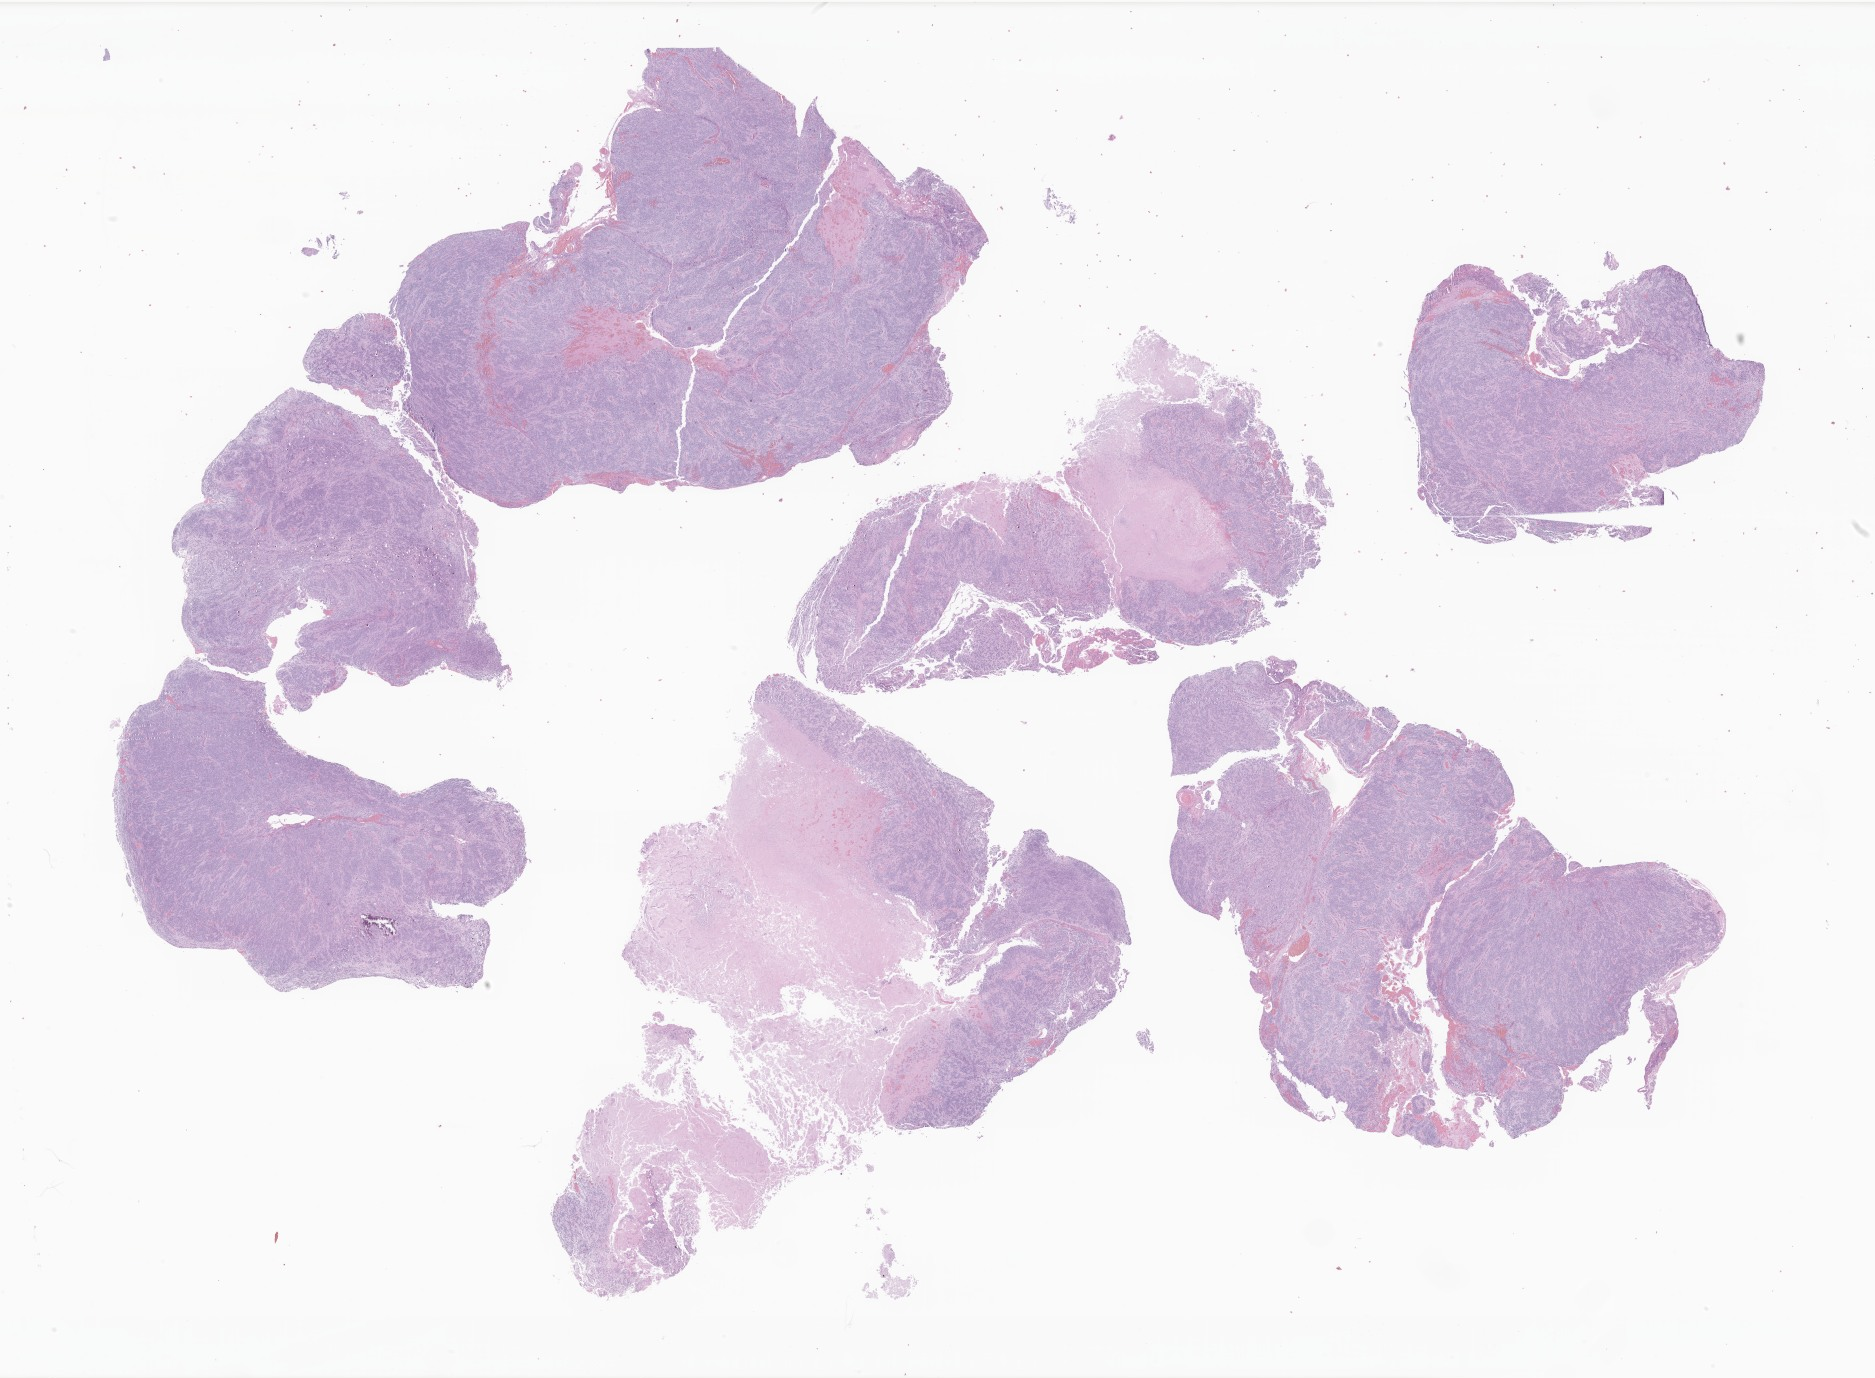
Haematoxylin and eosin whole-slide image of tumor tissue from the brain — whole scanned area (about 31.6 x 23.2 mm) shown as a low-resolution overview, formalin-fixed paraffin-embedded section. Patient: male, age 143 months (11 years 11 months).
Diagnosis (ICD-O-3 morphology term): Neoplasm, malignant.